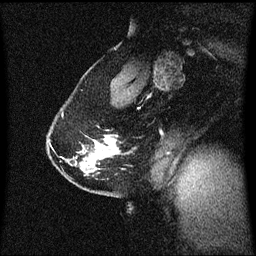
Breast MRI (dynamic contrast-enhanced), one sagittal slice. Slice 43 of 60 in the series (ordered by position). Dynamic contrast-enhanced series, image 2 of 3 at this slice position (ordered by acquisition). 1.5 T. TE 4.2 ms, TR 8.4 ms. 256 × 256 image matrix, field of view 210 × 210 mm. Female patient, age 40 years. Case-level facts recorded for this patient, not image findings: setting: breast cancer imaged before/during neoadjuvant chemotherapy; receptor status: triple-negative.
Structures marked on this image (semi-automatic segmentation, software-assisted and operator-edited):
- analysis volume of interest (the breast-tissue region the enhancement analysis was run in; not a lesion): box from (x=48, y=114) to (x=120, y=188) px
- tumour enhancement mask (voxels above the 70 % enhancement threshold inside the analysis volume of interest): (x=96, y=139)–(x=115, y=149)